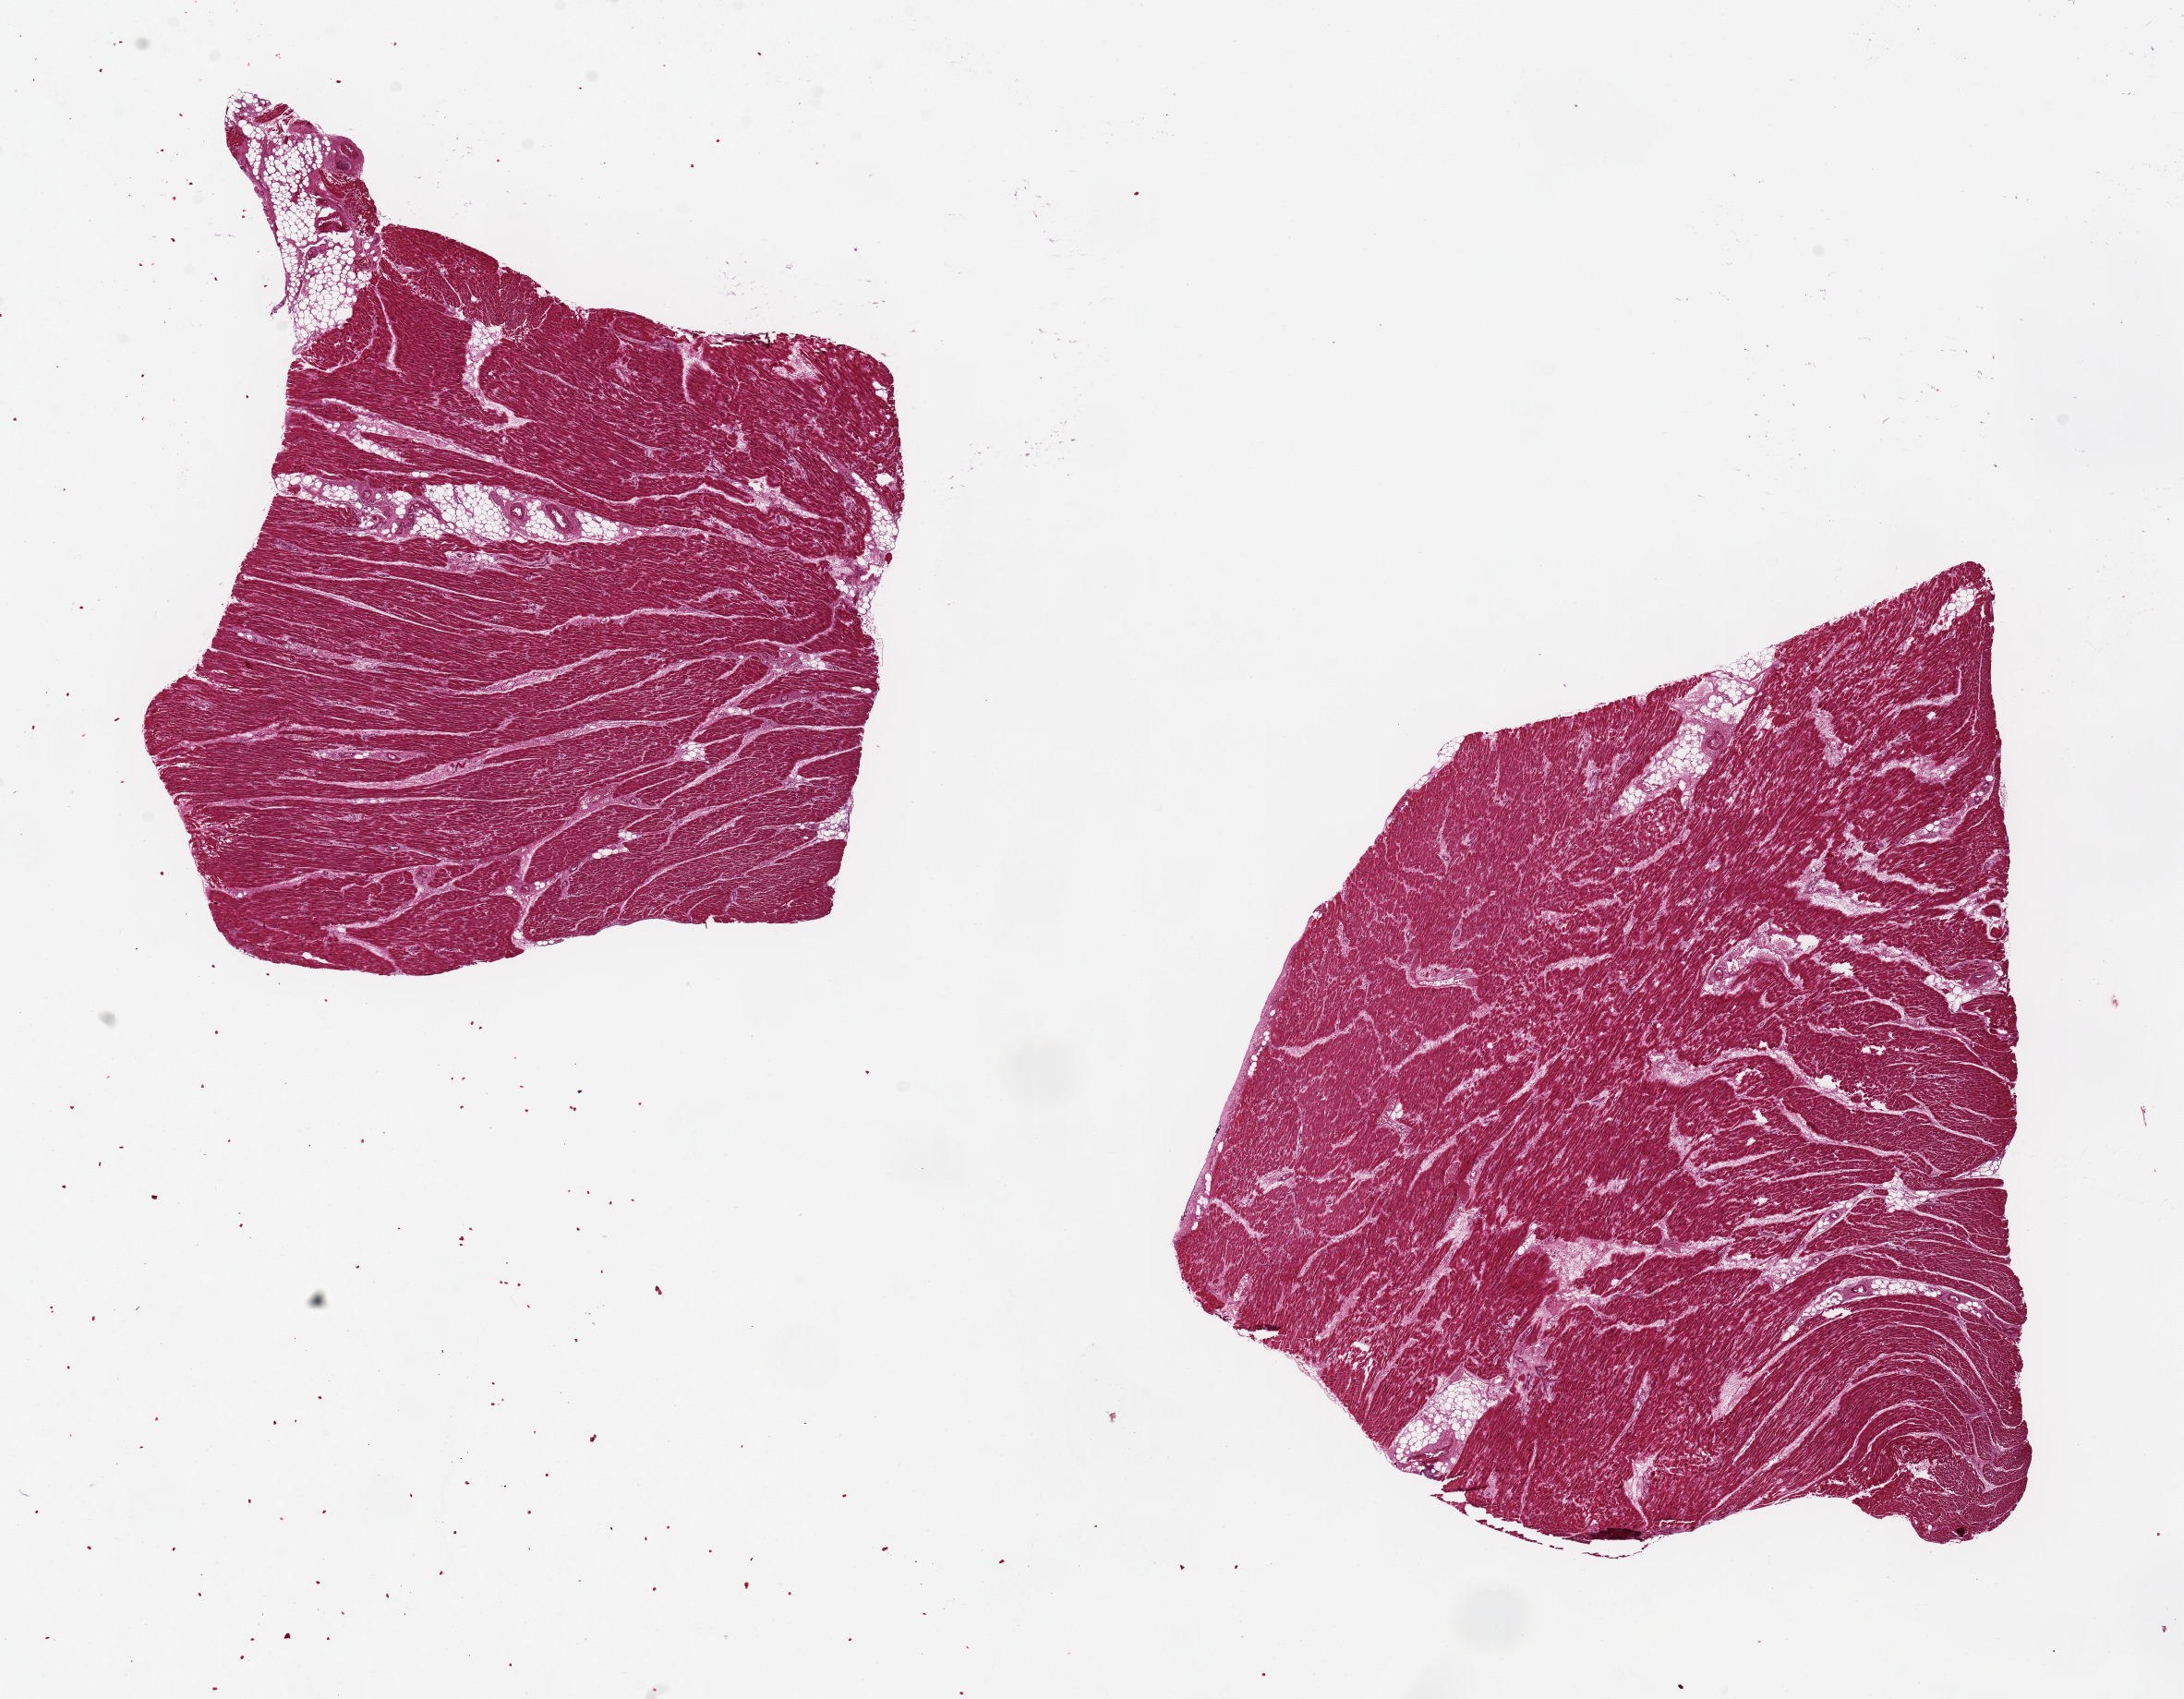
Digitized haematoxylin and eosin-stained section, shown as a low-resolution overview of the whole scanned area (about 18.7 x 14.6 mm), PAXgene-fixed paraffin-embedded (PFPE) section, sampled site (target tissue): heart, tissue donor sample. Donor sex: female.
• review note (as recorded): 2 aliquots, ~7x6mm. Mild ischemic changes